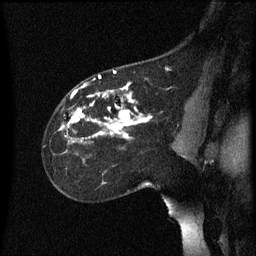
Breast MRI (dynamic contrast-enhanced), one sagittal slice. Position 40 of 60 along the scan axis. Dynamic contrast-enhanced series, image 2 of 3 at this slice position (ordered by acquisition). 1.5 T. TE 4.2 ms, TR 8.4 ms. 2.2 mm slice thickness. 256 × 256 image matrix, field of view 200 × 200 mm. Female patient, age 35 years. From the clinical record (not read from this slice): setting: breast cancer imaged before/during neoadjuvant chemotherapy; receptor status: HER2-positive.
Annotated regions visible in this slice (semi-automatically segmented with operator editing):
- analysis volume of interest (the breast-tissue region the enhancement analysis was run in; not a lesion): bounding box <44,72,178,173> (left, top, right, bottom; pixels)
- tumour enhancement mask (voxels above the 70 % enhancement threshold inside the analysis volume of interest): <60,72,153,143>